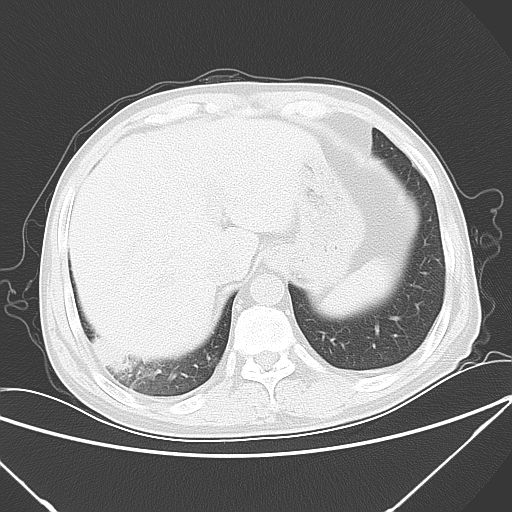
Chest CT, one axial slice; position 13 of 57 along the scan axis; lung window (W 1500 / L -600 HU); 5 mm slice thickness; 512 × 512 image matrix, field of view 364 × 364 mm. Male patient, age 54 years. Case-level facts recorded for this patient, not image findings: clinical TNM (as recorded): T2 N1 M0.
Annotated regions visible in this slice (bounding box drawn by a radiologist):
- lung tumour (recorded histology: adenocarcinoma): bounding box (x1, y1, x2, y2) in pixels: (89, 331, 131, 371)